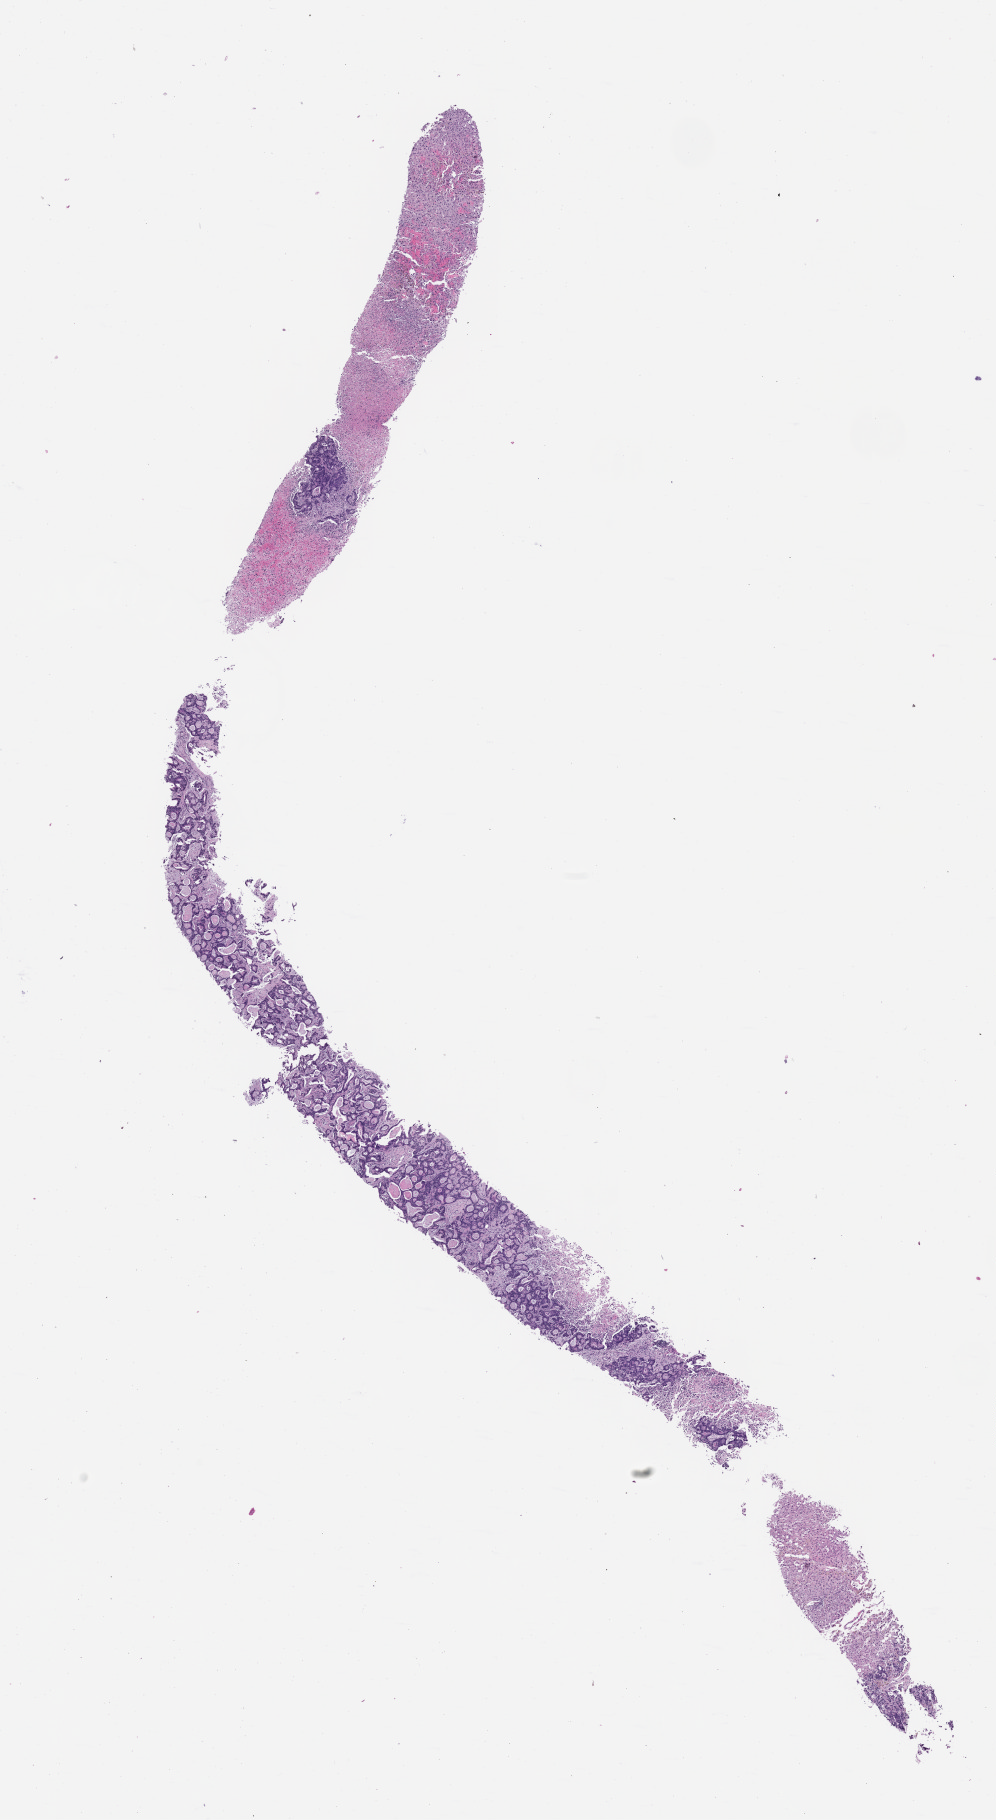
Whole-slide image, haematoxylin and eosin stain of the patient's (originator) tumor tissue, low-resolution overview of the scanned area, about 8.0 x 14.6 mm; FFPE section; originating tumor site category: colon. Patient male; aged 55.
* diagnosis: Colon Adenocarcinoma